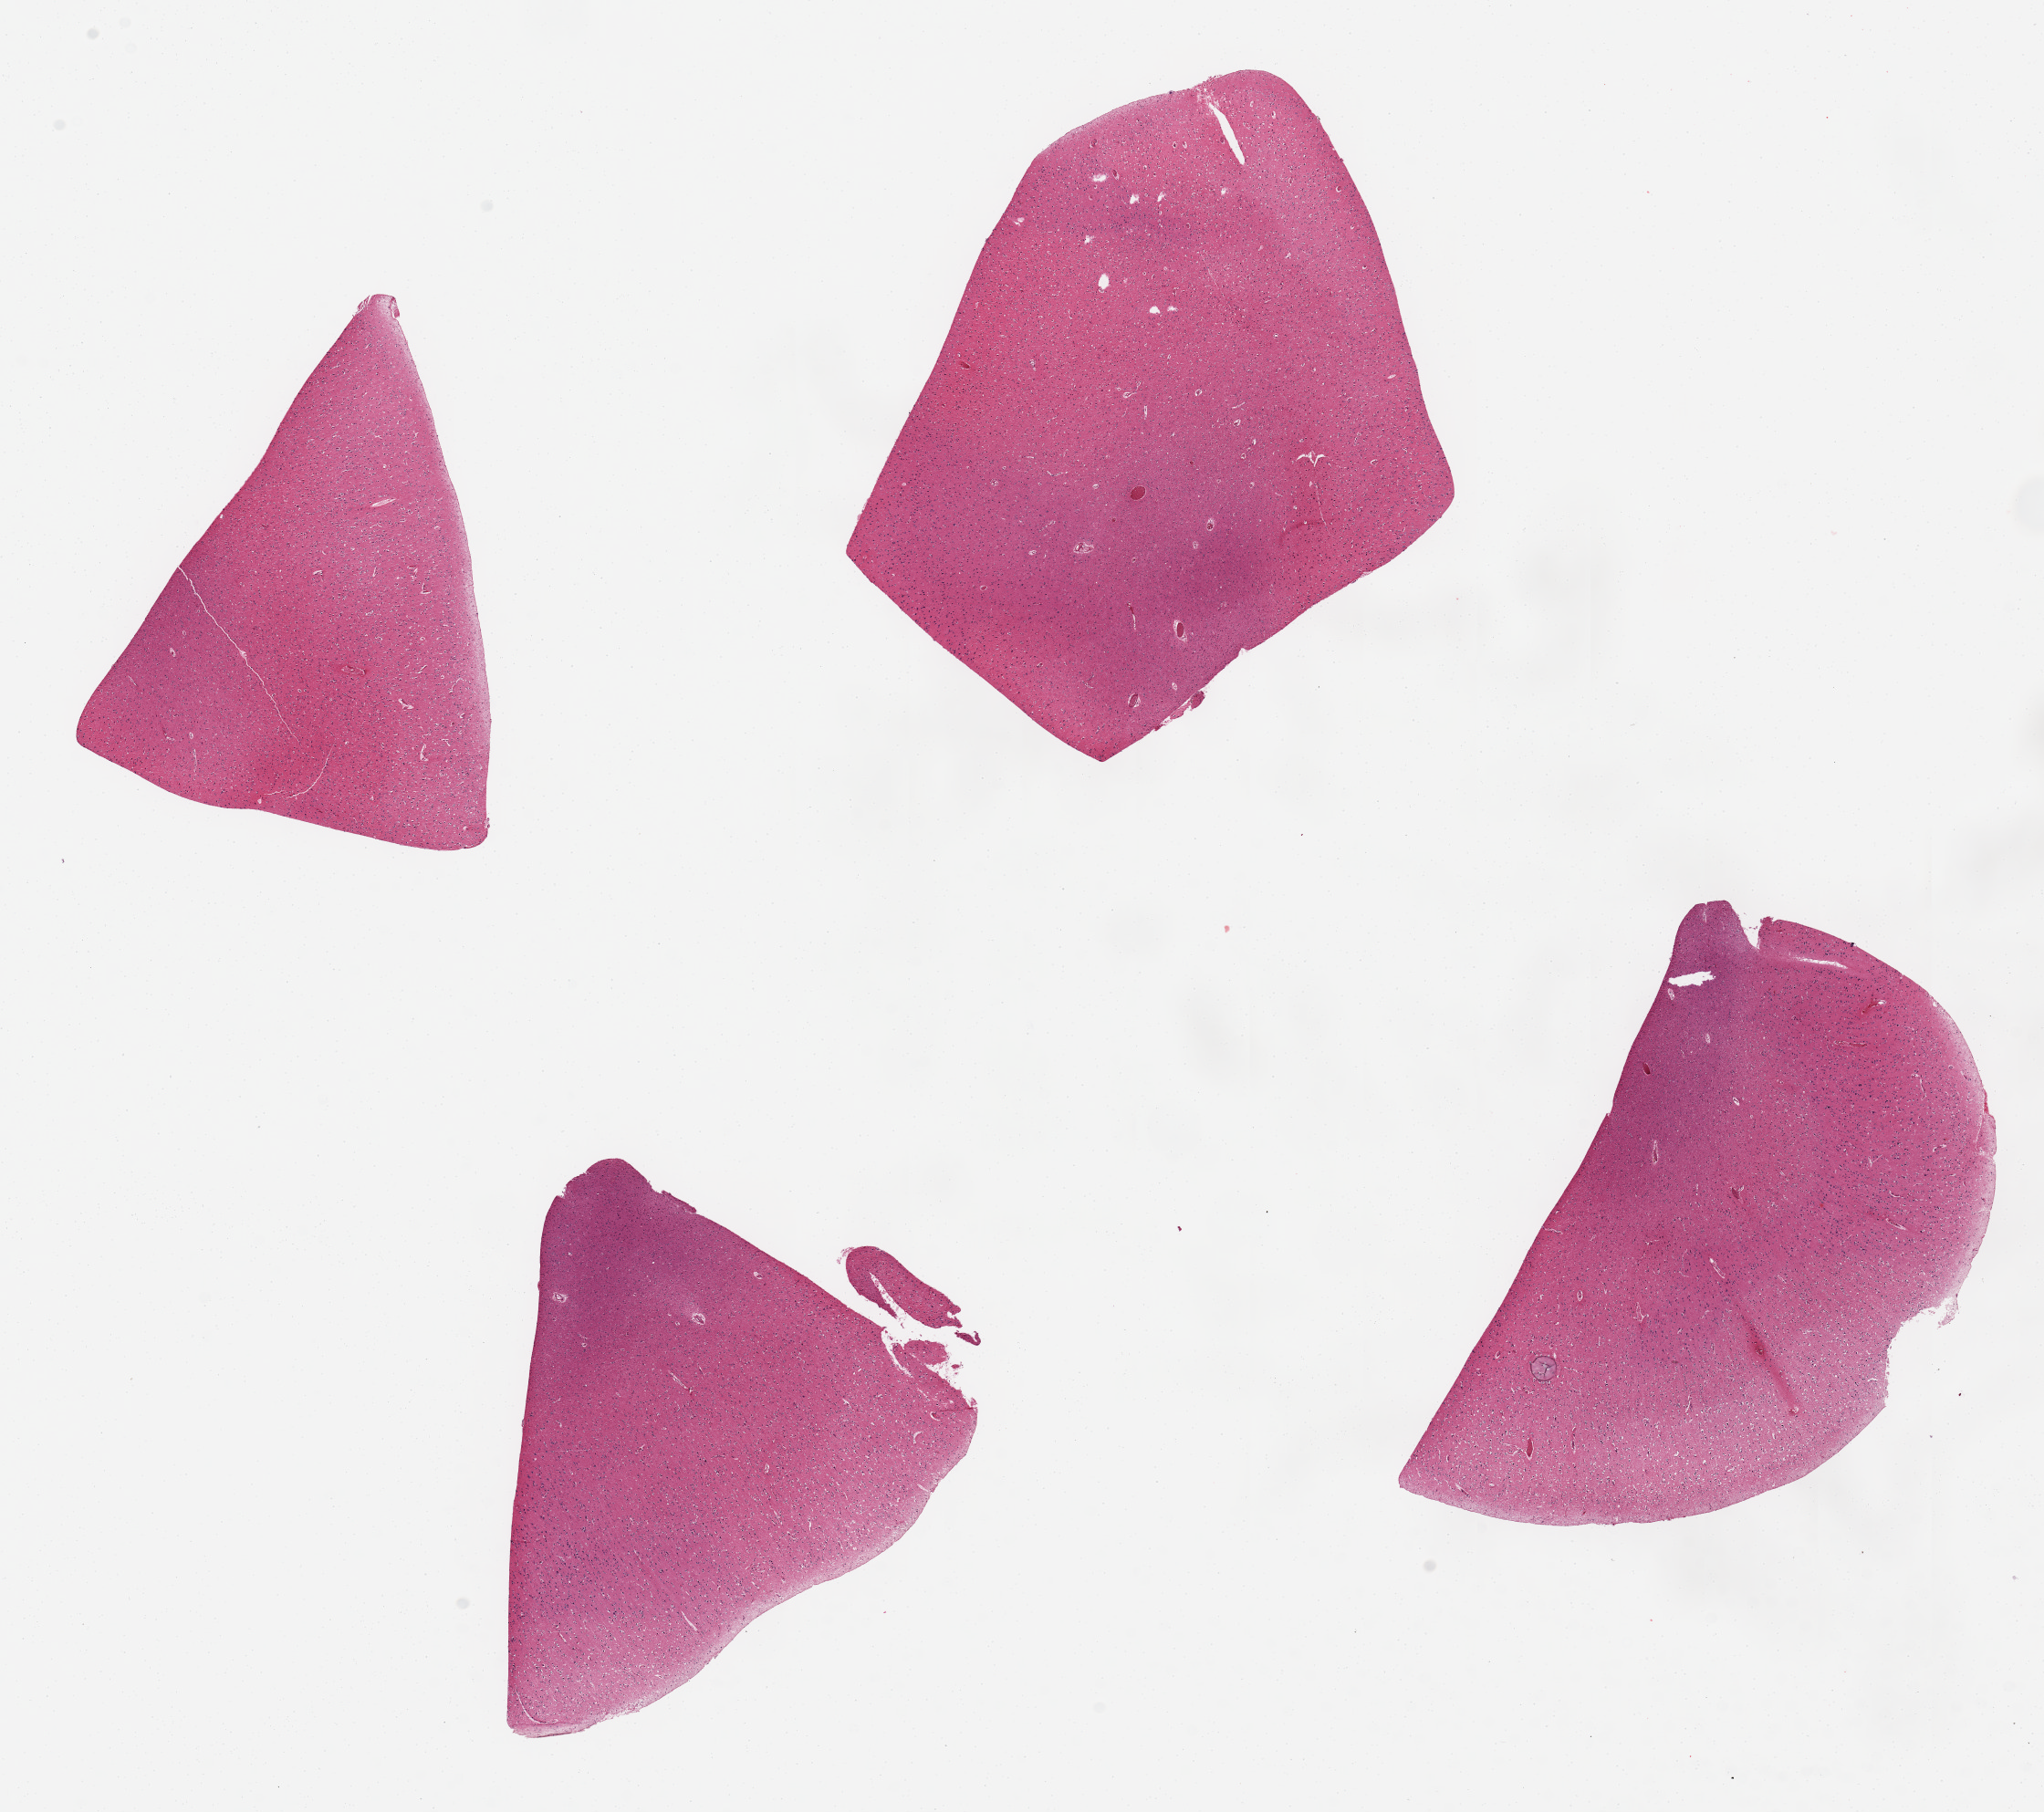
Whole-slide image, hematoxylin and eosin (H&E) stain — whole scanned area (about 17.7 x 15.7 mm) shown as a low-resolution overview, PAXgene-fixed paraffin-embedded (PFPE) section, target tissue: cerebral cortex, donor tissue sample.
Reviewer comment on this tissue sample: 4 pieces up to 5x5 mm.